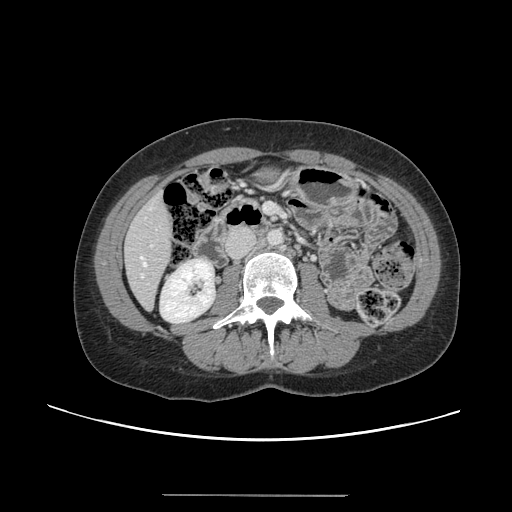
Contrast-enhanced abdominal CT, one axial slice; slice 40 of 144 in the series (ordered by position); 120 kVp; intravenous contrast given; soft-tissue window (W 400 / L 40 HU); 2.5 mm slice thickness; 512 × 512 image matrix, field of view 380 × 380 mm. Female patient, age 53 years. From the clinical record (not read from this slice): diagnosis: colorectal cancer liver metastases, imaged before liver resection; multiple liver metastases: yes; largest metastasis: 1.1 cm; chemotherapy before resection: no.
Outlined on this slice (manually delineated by an expert):
- hepatic veins: bounding box [x1, y1, x2, y2] px = [141, 256, 146, 277]
- liver: [125, 194, 172, 308]
- planned liver remnant (the part of the liver to remain after resection): [125, 194, 172, 308]
- portal vein (with intrahepatic branches): [150, 244, 154, 248]